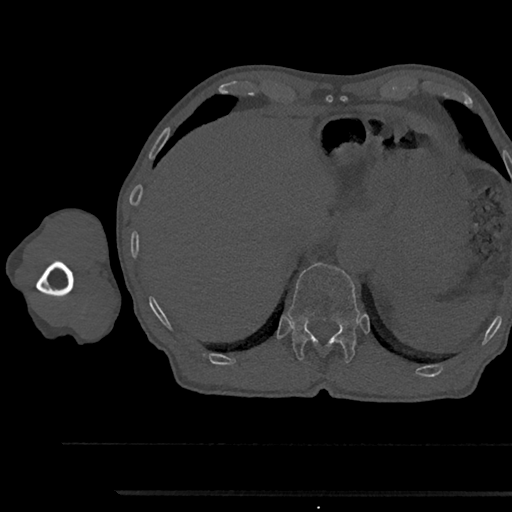
CT including the spine, one axial slice. Position 733 of 797 along the scan axis. Reconstruction kernel Br40s/3. Bone window (W 1800 / L 400 HU). 512 × 512 image matrix. Male patient, age 79 years. From the clinical record (not read from this slice): primary cancer: prostate.
Structures marked on this image (semi-automatically segmented with operator editing):
- T12 vertebra: bounding box <287,262,359,363> (left, top, right, bottom; pixels)